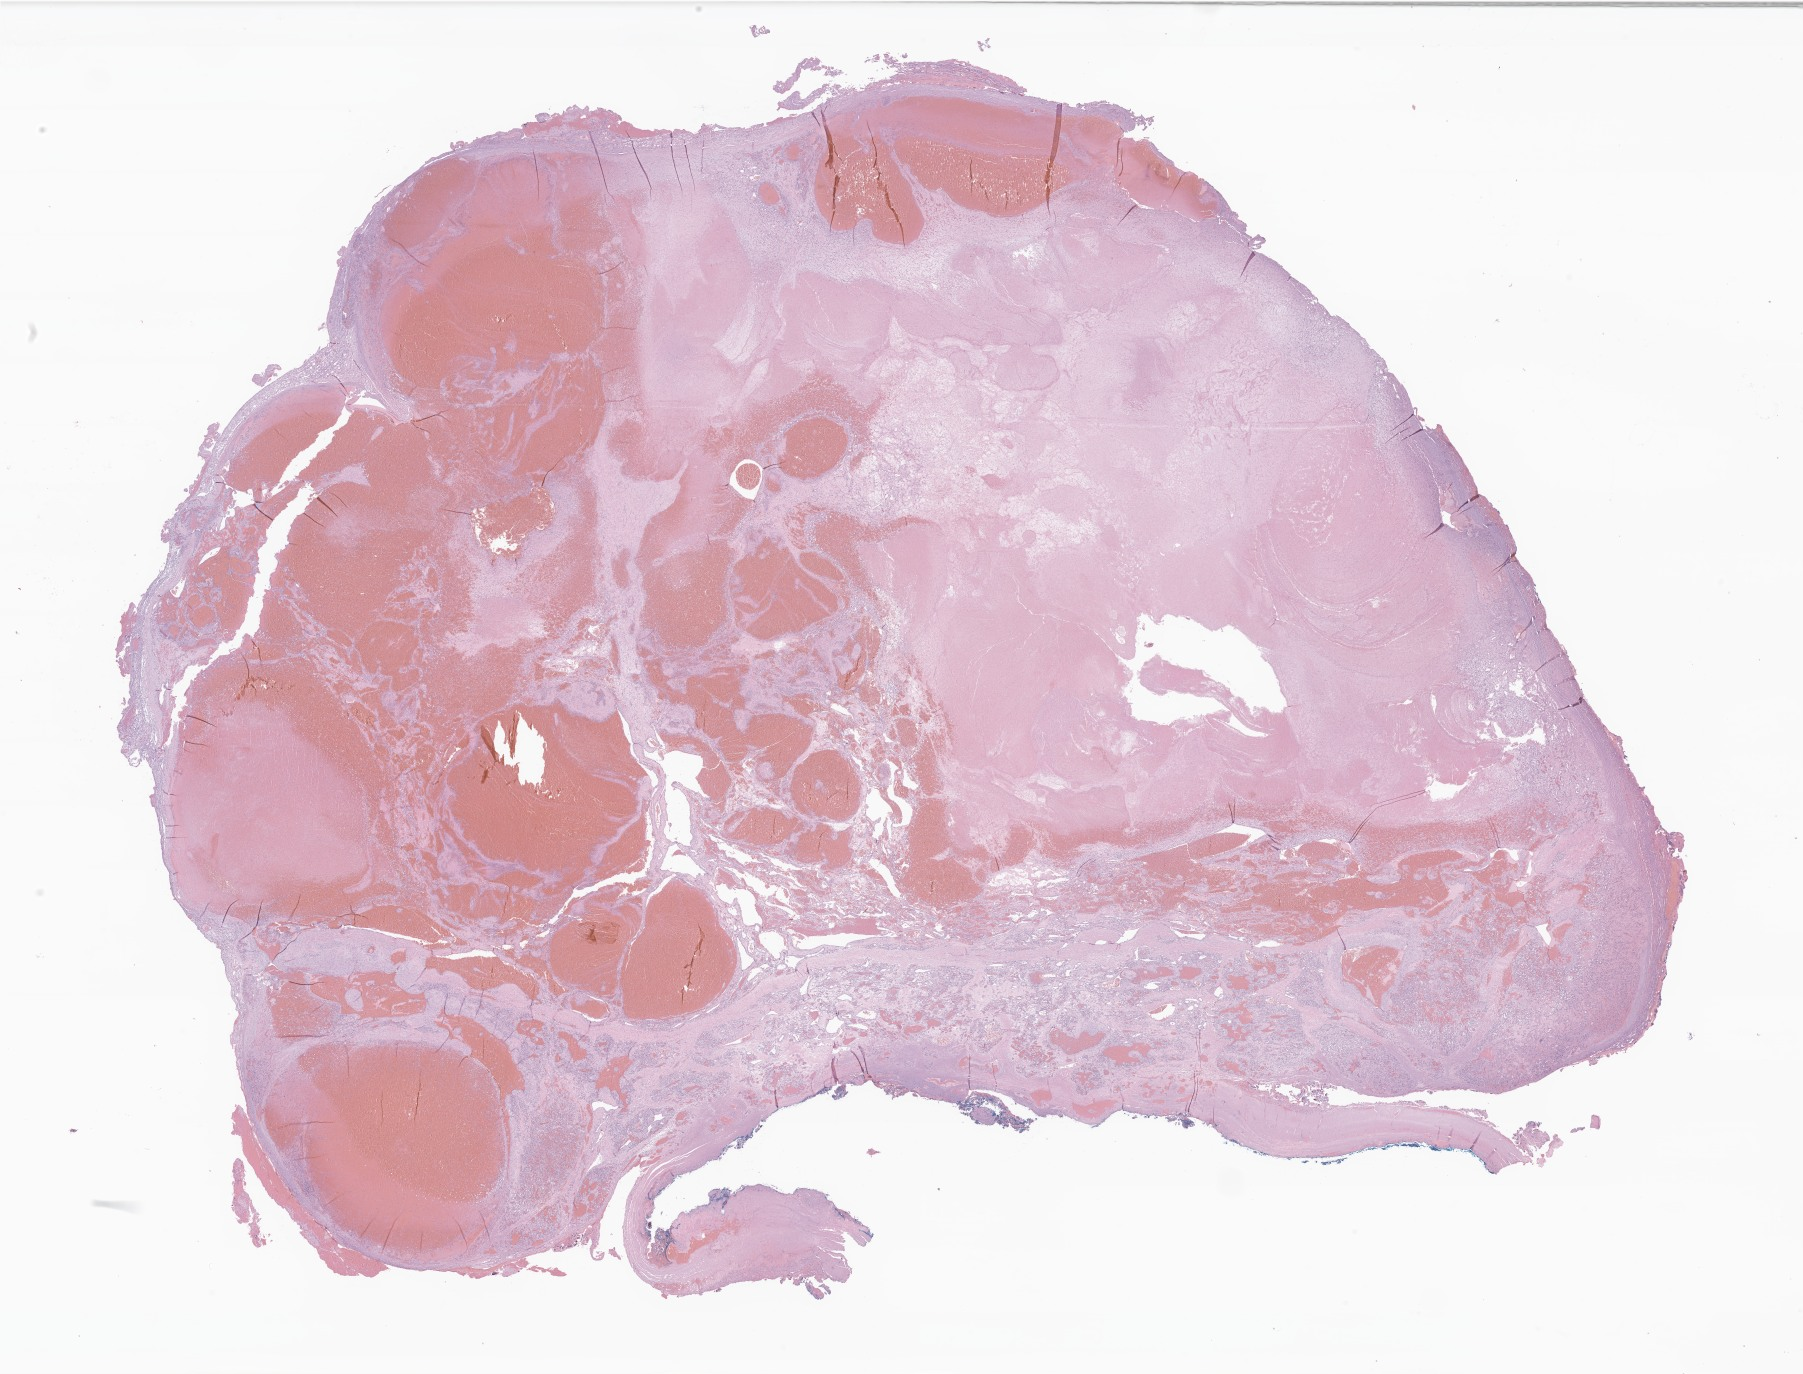
Whole-slide image, hematoxylin and eosin (H&E) stain of tumor tissue from the brain, a low-resolution overview of the entire scanned area, about 30.4 x 23.2 mm. Formalin-fixed paraffin-embedded section. Patient: male, age 198 months (16 years 6 months).
Recorded diagnosis: Hemangioma, NOS.